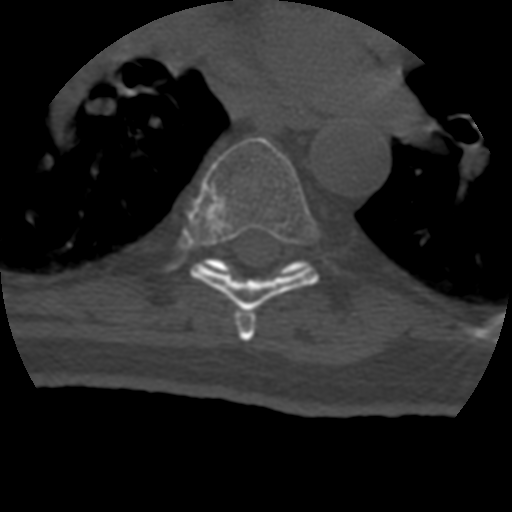
CT including the spine, one axial slice; position 277 of 399 along the scan axis; 120 kVp; bone window (W 1800 / L 400 HU); 1.25 mm slice thickness; 512 × 512 image matrix, field of view 160 × 160 mm. Patient age 69 years. Case-level facts recorded for this patient, not image findings: primary cancer: prostate.
Outlined on this slice (semi-automatic segmentation, software-assisted and operator-edited):
- T6 vertebra: bounding box <234,311,256,342> (left, top, right, bottom; pixels)
- T7 vertebra: <186,137,320,311>
- T8 vertebra: <200,257,309,274>